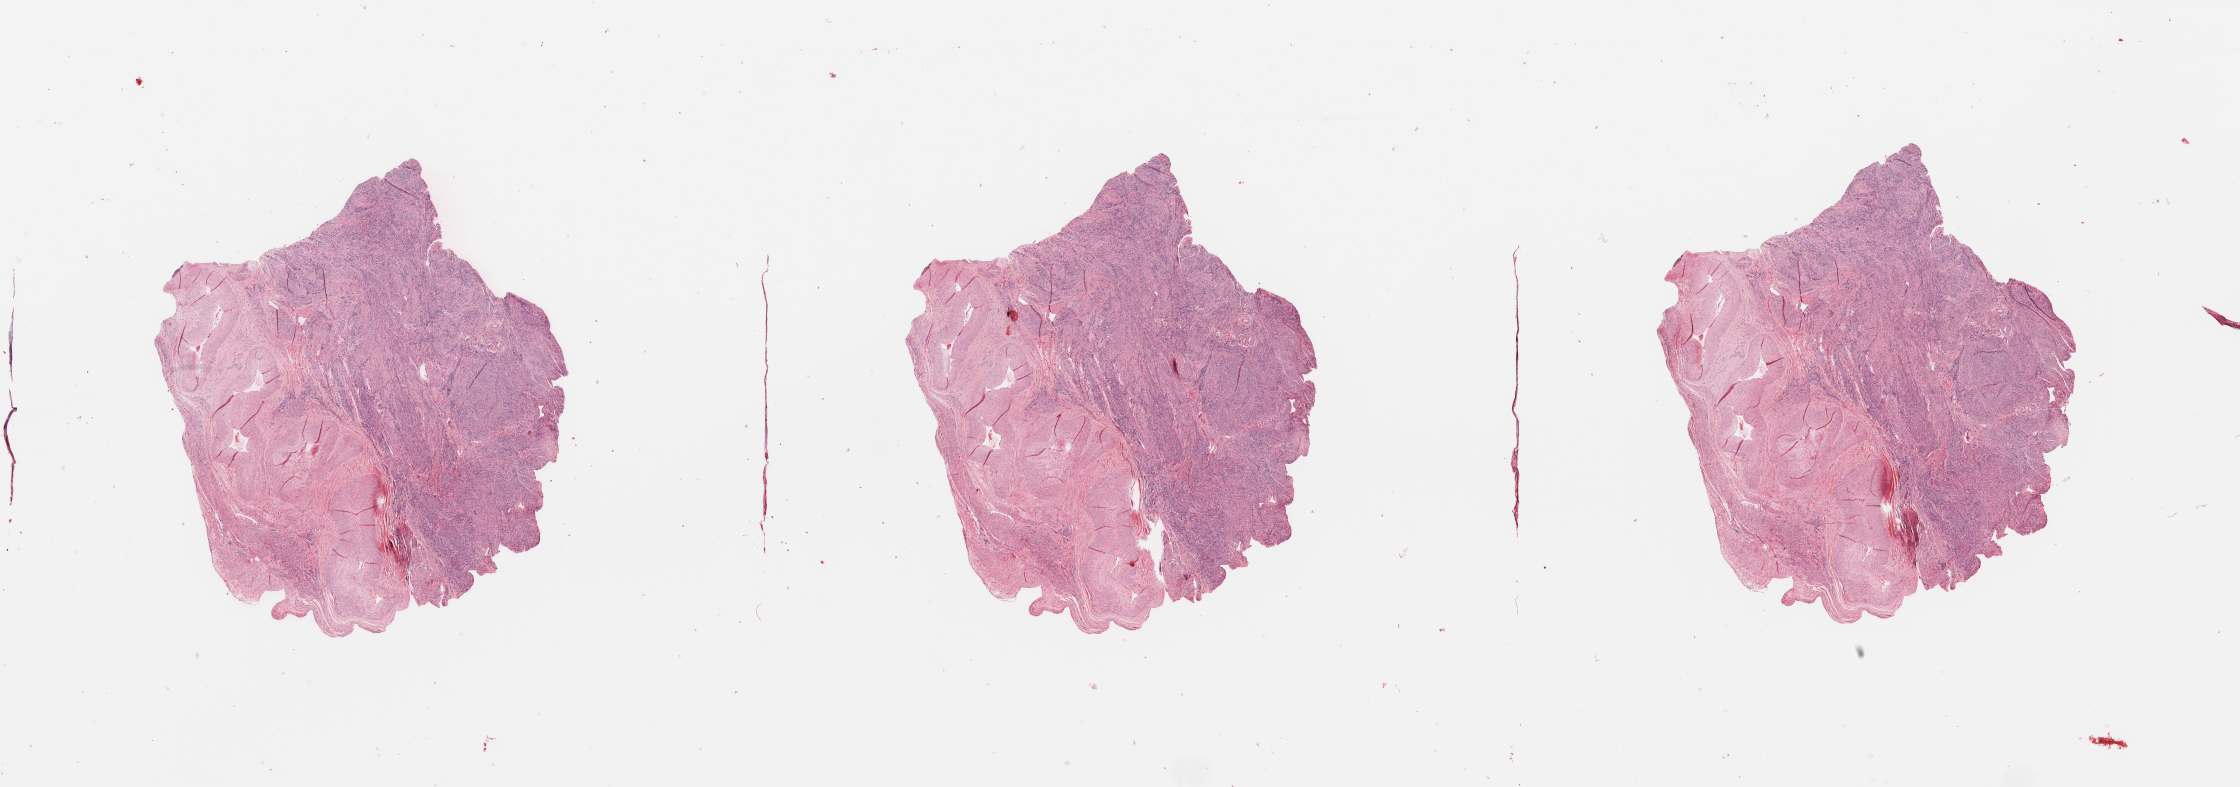
H&E-stained whole-slide image — shown as a low-resolution overview of the whole scanned area (about 35.4 x 12.5 mm), uterus, normal (non-tumour) tissue. Female, 53 y/o.
This section: normal (non-tumour) tissue from the same patient. Patient diagnosis: Endometrioid adenocarcinoma, NOS.